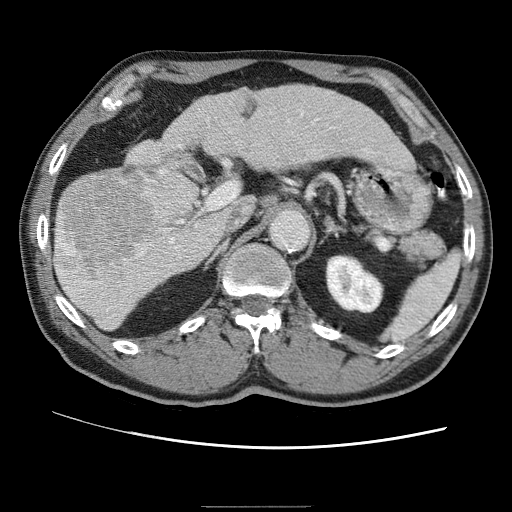
Contrast-enhanced abdominal CT (liver protocol), one axial slice. Position 29 of 75 along the scan axis. One of 2 acquisitions stored at this slice position. Soft-tissue window (W 400 / L 40 HU). 2.5 mm slice thickness. 512 × 512 image matrix, field of view 360 × 360 mm. From the clinical record (not read from this slice): diagnosis: hepatocellular carcinoma (patient treated with transarterial chemoembolisation; whether this scan precedes or follows treatment is not stated here); TNM stage (as recorded): Stage-II; Child-Pugh class: A.
Structures marked on this image (semi-automatically segmented with operator editing):
- liver parenchyma outside the tumour (the mass and vessels are separate outlines, so this box may not span the whole liver): bounding box <56,86,409,328> (left, top, right, bottom; pixels)
- mass: <56,183,148,281>
- liver vessels: <61,119,294,280>